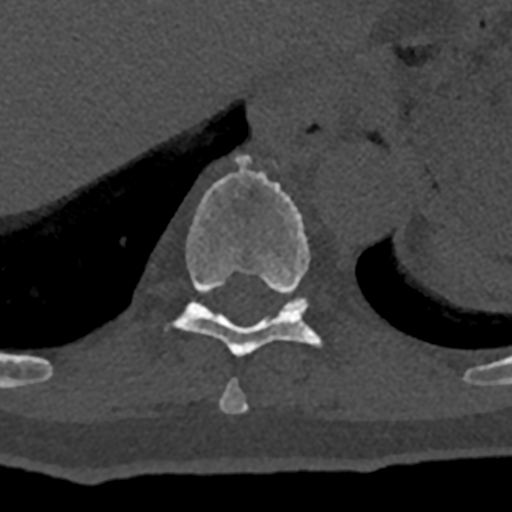
CT including the spine, one axial slice. Reconstruction kernel Br40s/3. Bone window (W 1800 / L 400 HU). 0.5 mm slice thickness. 512 × 512 image matrix, field of view 160 × 160 mm. Male patient, age 74 years. Case-level facts recorded for this patient, not image findings: primary cancer: renal; vertebrae with lytic lesions (as recorded): T10, L1, L2, L3, L4, L5.
Structures marked on this image (semi-automatically segmented with operator editing):
- T10 vertebra: box from (x=173, y=154) to (x=322, y=357) px
- T11 vertebra: (x=283, y=298)–(x=309, y=311)
- T9 vertebra: (x=219, y=379)–(x=249, y=413)